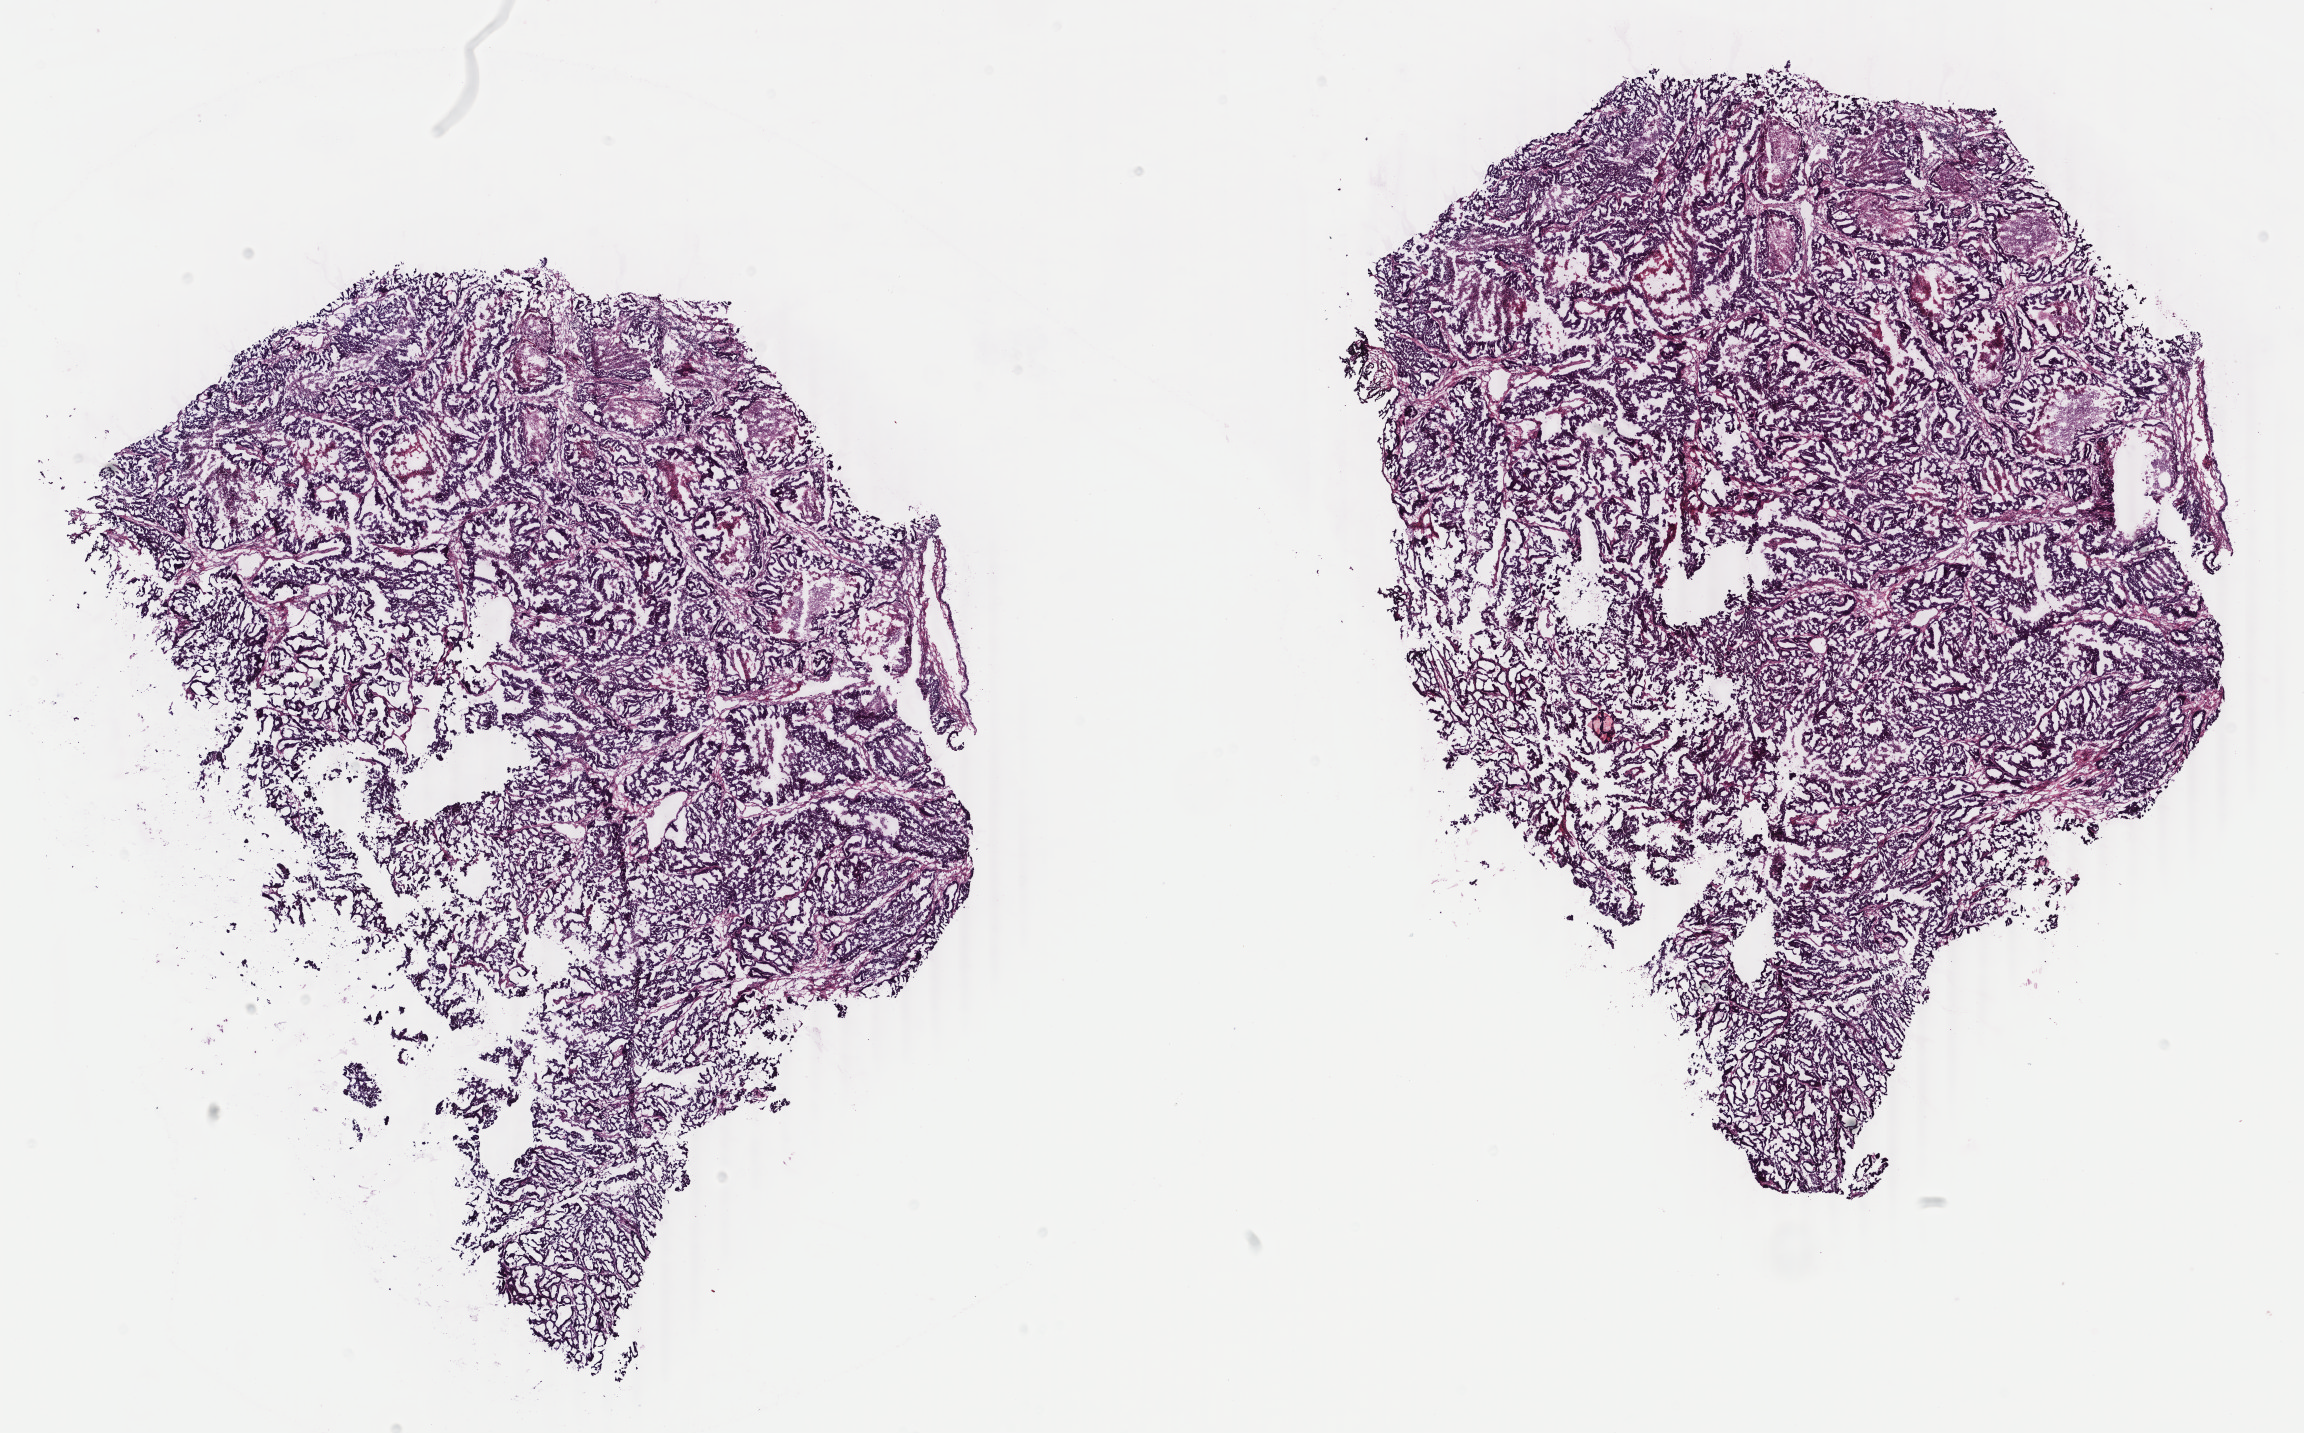
Digitized H&E-stained tissue section (whole slide) — whole scanned area (about 18.3 x 11.4 mm, from a 40x scan) shown as a low-resolution overview. Frozen section from the top of the tissue portion. Primary tumour sample from the uterus. Female patient; age at initial diagnosis 57 years. Histologic grade: G2 (moderately differentiated). Pathologist review of this section (percent, as recorded): tumour cells 85%, tumour nuclei 80%, normal cells 0%, stromal cells 0%, necrosis 15%. Inflammatory infiltration, as recorded: lymphocyte infiltration 0%, monocyte infiltration 0%, neutrophil infiltration 0%.
FIGO stage: II. Pathologic diagnosis: Endometrioid adenocarcinoma, NOS. Lymph nodes positive (case pathology): 0 of 16 examined.